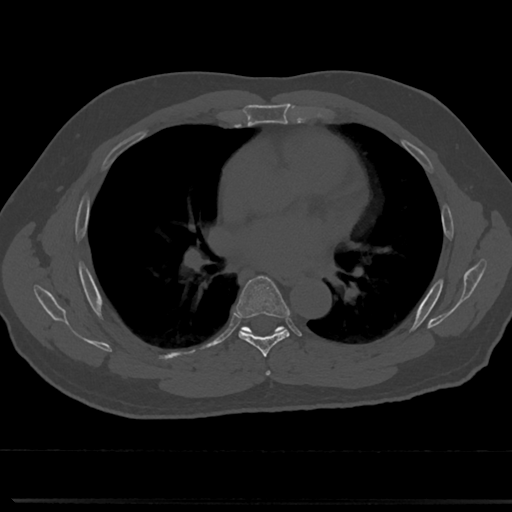
CT including the spine, one axial slice; position 443 of 817 along the scan axis; reconstruction kernel Br40s/3; 120 kVp; bone window (W 1800 / L 400 HU); 0.5 mm slice thickness; 512 × 512 image matrix, field of view 355 × 355 mm. Male patient, age 61 years. Case-level facts recorded for this patient, not image findings: primary cancer: prostate.
Annotated regions visible in this slice (semi-automatically segmented with operator editing):
- T5 vertebra: bounding box <264,357,273,377> (left, top, right, bottom; pixels)
- T6 vertebra: <220,277,309,353>